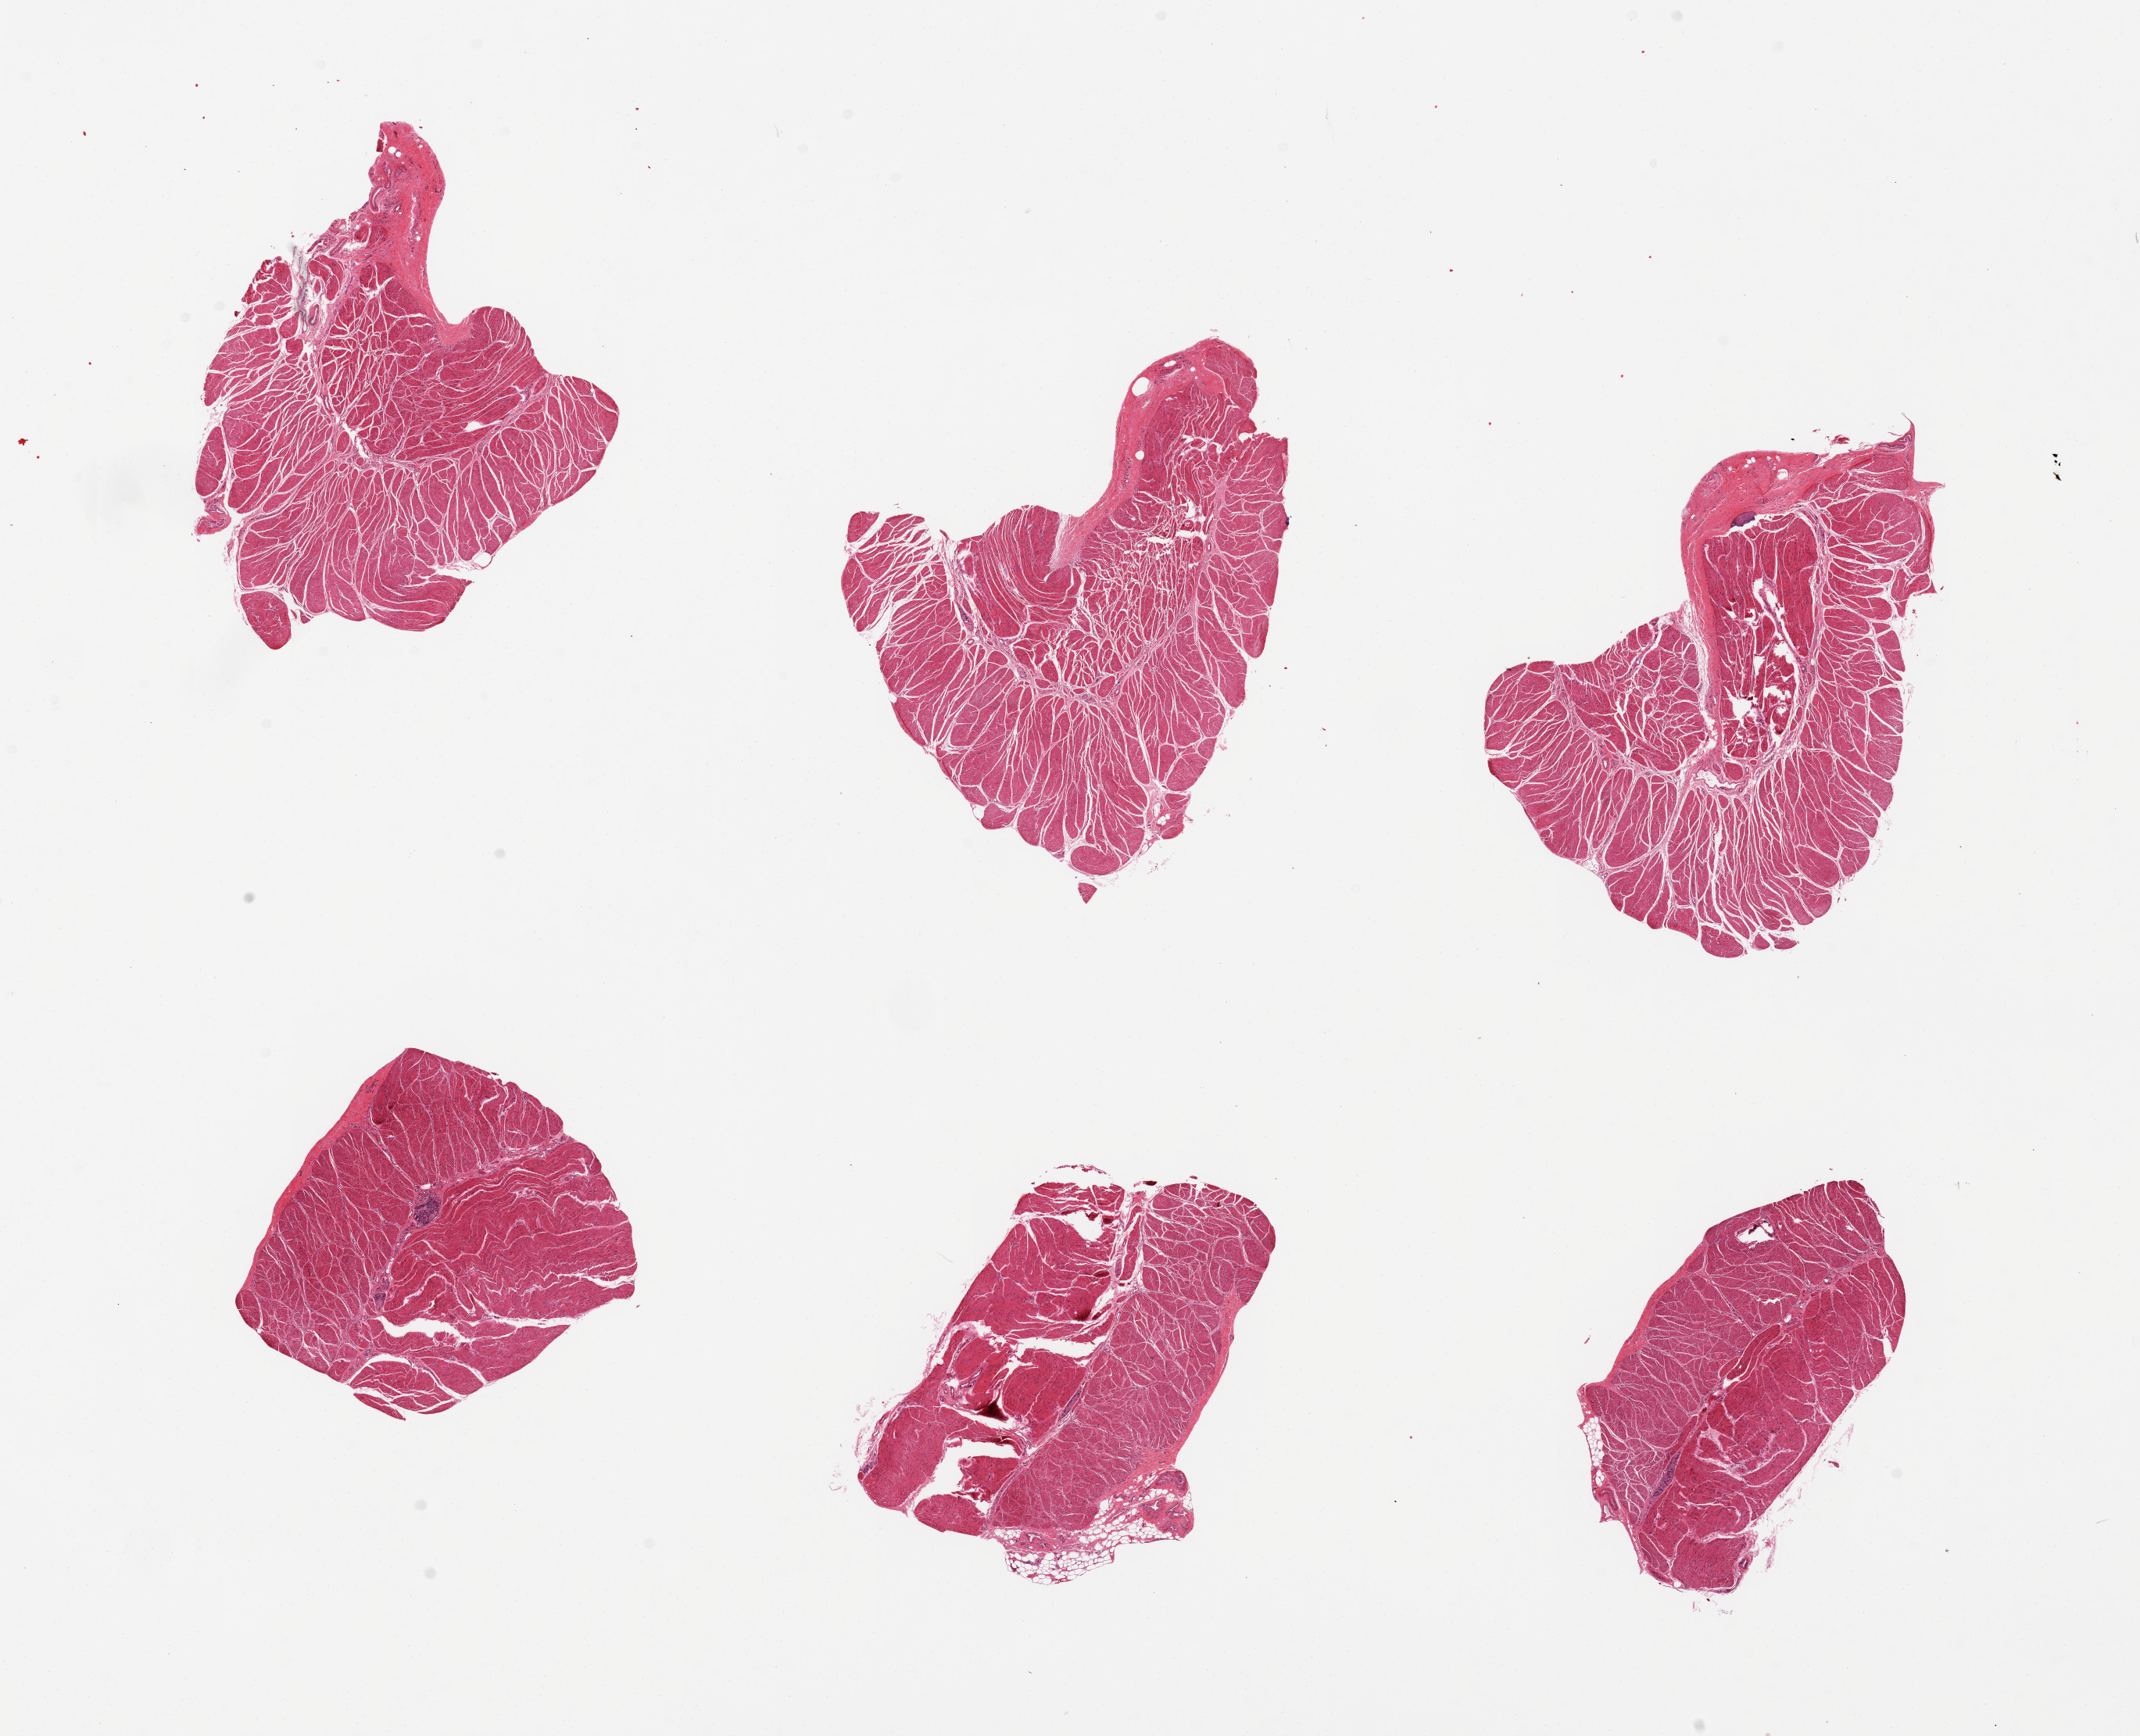
H&E whole-slide image, brightfield, a low-resolution overview of the entire scanned area, about 21.7 x 17.6 mm. PAXgene-fixed, paraffin-embedded tissue. Section of esophageal muscle (target tissue). Donor tissue sample. Donor sex: female.
Reviewer comment on this tissue sample: 6 pieces, well trimmed.